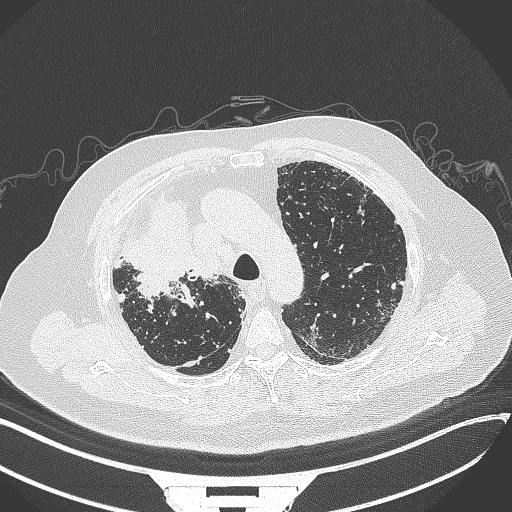
Chest CT, one axial slice. Slice 264 of 384 in the series (ordered by position). Reconstruction kernel B70f. Lung window (W 1500 / L -600 HU). 1 mm slice thickness. 512 × 512 image matrix, field of view 400 × 400 mm. Male patient, age 69 years. Case-level facts recorded for this patient, not image findings: clinical TNM (as recorded): T4 N3 M1.
Structures marked on this image (bounding box drawn by a radiologist):
- lung tumour (recorded histology: adenocarcinoma): bounding box [x1, y1, x2, y2] px = [119, 199, 212, 305]